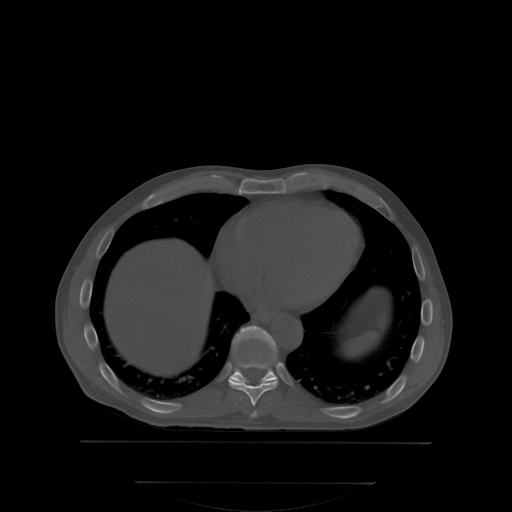
CT including the spine, one axial slice; slice 201 of 350 in the series (ordered by position); bone window (W 1800 / L 400 HU); 512 × 512 image matrix, field of view 500 × 500 mm. Patient: male, 58 years. Case-level facts recorded for this patient, not image findings: primary cancer: prostate; vertebrae with lytic lesions (as recorded): L1.
Structures marked on this image (semi-automatic segmentation, software-assisted and operator-edited):
- T10 vertebra: bounding box <230,327,277,382> (left, top, right, bottom; pixels)
- T8 vertebra: <253,410,257,415>
- T9 vertebra: <229,362,279,405>